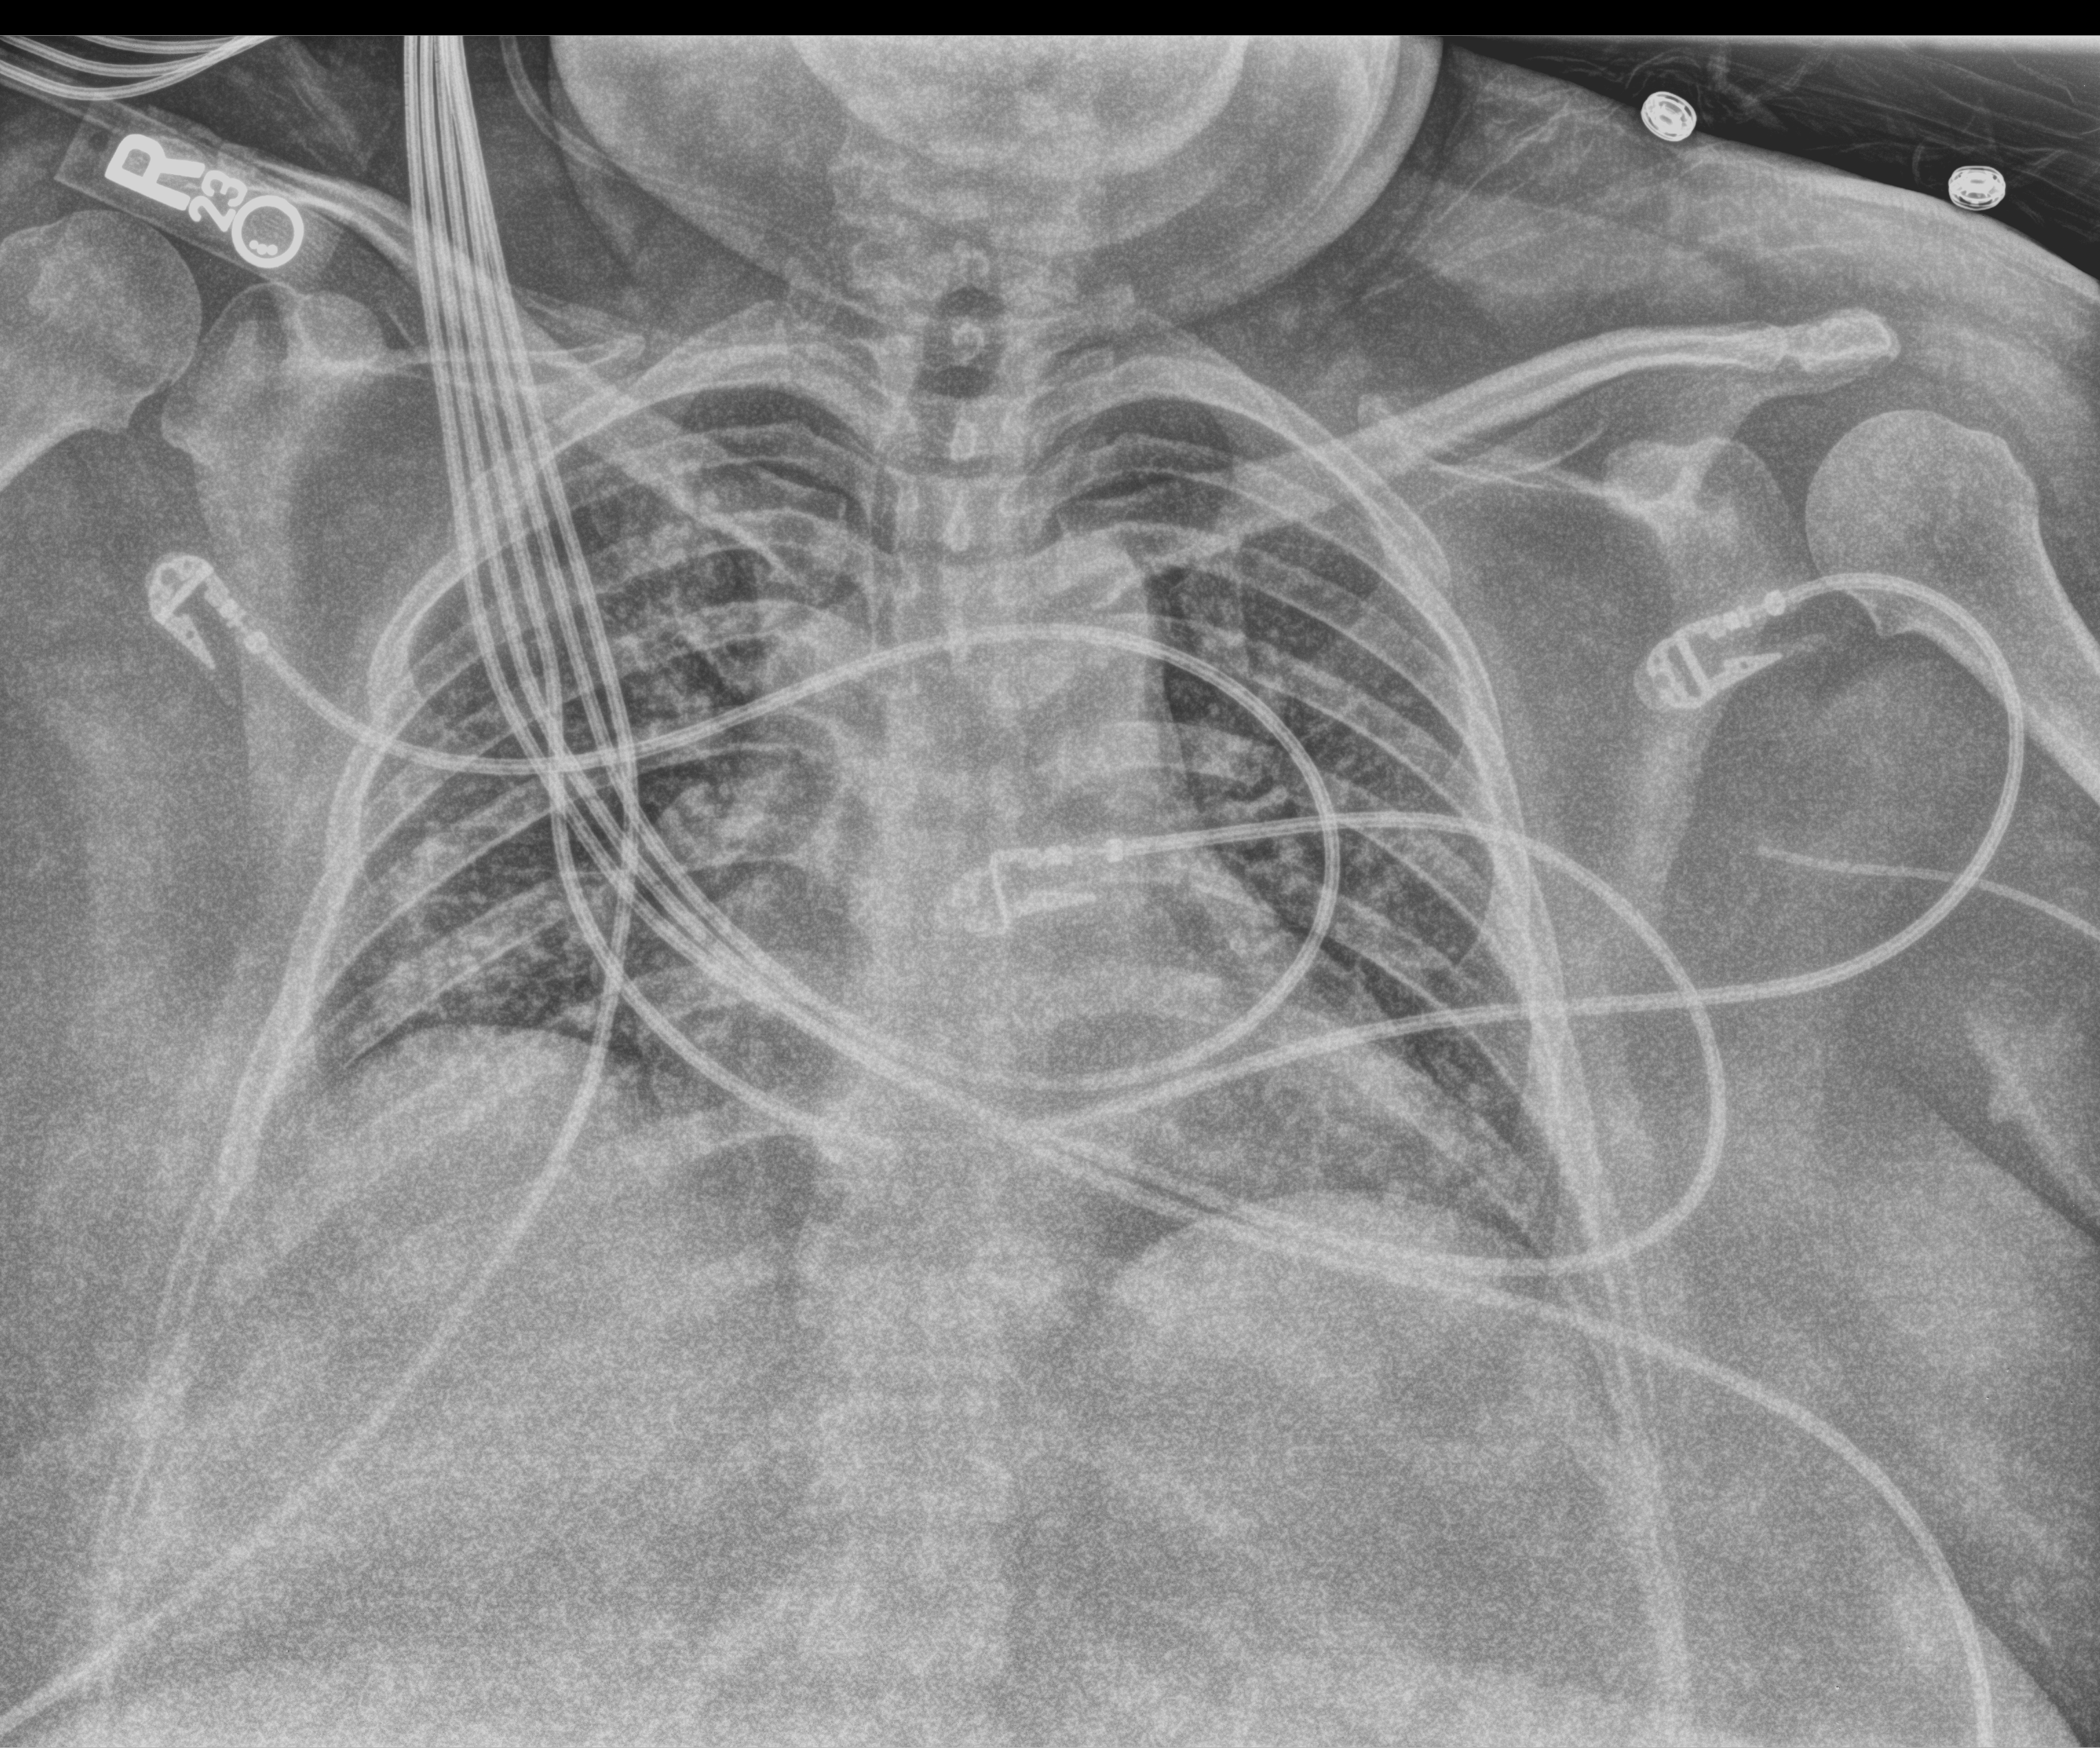
Bedside chest radiograph (computed radiography); anteroposterior (AP) projection. Patient hospitalised with COVID-19; female, aged 18–59 years.
Admission-level facts for this patient (not findings on this image; timing relative to this image not recorded):
- chronic kidney disease (admission record): no
- mechanically ventilated during this hospital stay: yes